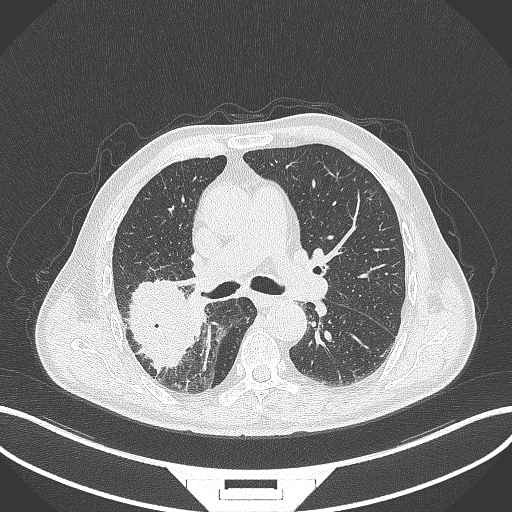
Chest CT, one axial slice; position 247 of 429 along the scan axis; lung window (W 1500 / L -600 HU); 1 mm slice thickness; 512 × 512 image matrix, field of view 400 × 400 mm. Male patient, age 72 years. From the clinical record (not read from this slice): clinical TNM (as recorded): T3 N2 M0.
Structures marked on this image (rectangle marked by the reading radiologist):
- lung tumour (recorded histology: adenocarcinoma): bounding box <120,278,198,370> (left, top, right, bottom; pixels)